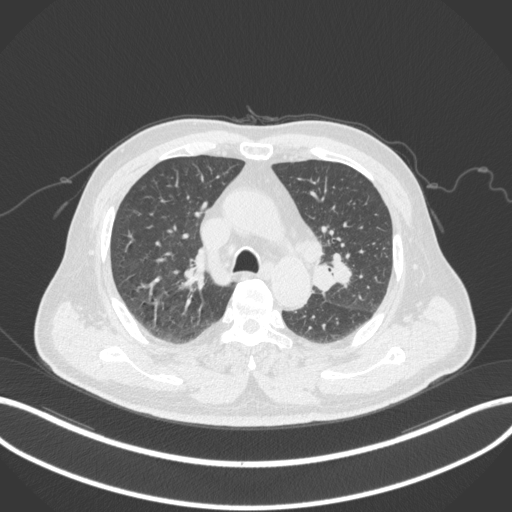
Chest CT, one axial slice; position 203 of 286 along the scan axis; 120 kVp; lung window (W 1500 / L -600 HU); 1 mm slice thickness; 512 × 512 image matrix, field of view 400 × 400 mm. Male patient, age 67 years. Case-level facts recorded for this patient, not image findings: clinical TNM (as recorded): T2a N1 M0; histopathological grade: G3.
Structures marked on this image (bounding box drawn by a radiologist):
- lung tumour (recorded histology: adenocarcinoma): bounding box <310,253,354,297> (left, top, right, bottom; pixels)